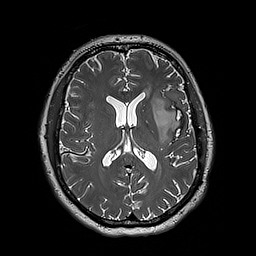
Brain MRI from a brain-tumour surgery series, one axial slice. Position 93 of 192 along the scan axis. 1 mm slice thickness. 256 × 256 image matrix, field of view 250 × 250 mm. Case-level facts recorded for this patient, not image findings: histopathology: Astrocytoma; WHO grade: 3; IDH mutation: yes.
Annotated regions visible in this slice (outlined manually by an expert reader):
- tumour: bounding box [x1, y1, x2, y2] px = [152, 94, 181, 144]